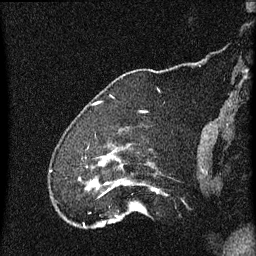
Breast MRI (dynamic contrast-enhanced), one sagittal slice. Position 13 of 60 along the scan axis. Dynamic contrast-enhanced series, image 2 of 4 at this slice position (ordered by acquisition). 1.5 T. TE 4.2 ms, TR 8 ms. 2 mm slice thickness. 256 × 256 image matrix. Female patient, age 52 years.
Annotated regions visible in this slice (semi-automatically segmented with operator editing):
- analysis volume of interest (the breast-tissue region the enhancement analysis was run in; not a lesion): bounding box (x1, y1, x2, y2) in pixels: (79, 148, 162, 219)
- tumour enhancement mask (voxels above the 70 % enhancement threshold inside the analysis volume of interest): (92, 158, 111, 187)